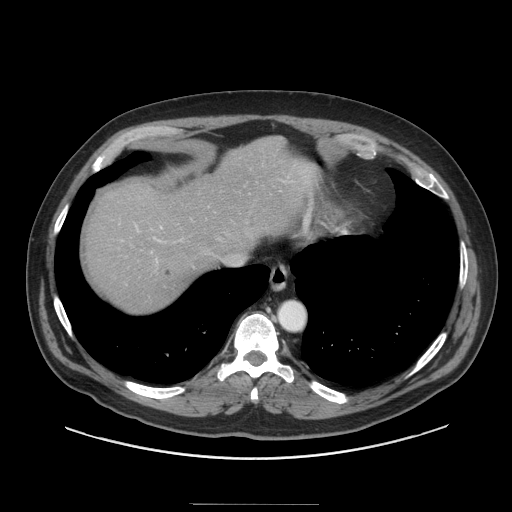
Contrast-enhanced abdominal CT (liver protocol), one axial slice. Slice 79 of 91 in the series (ordered by position). Reconstruction kernel STANDARD. Soft-tissue window (W 400 / L 40 HU). 2.5 mm slice thickness. 512 × 512 image matrix, field of view 440 × 440 mm. From the clinical record (not read from this slice): diagnosis: hepatocellular carcinoma (patient treated with transarterial chemoembolisation; whether this scan precedes or follows treatment is not stated here); TNM stage (as recorded): Stage-I; Child-Pugh class: A; tumour nodularity: uninodular; tumour size: 4 cm.
Annotated regions visible in this slice (semi-automatically segmented with operator editing):
- liver parenchyma outside the tumour (the mass and vessels are separate outlines, so this box may not span the whole liver): bounding box [x1, y1, x2, y2] px = [84, 136, 316, 312]
- liver vessels: [137, 227, 162, 261]